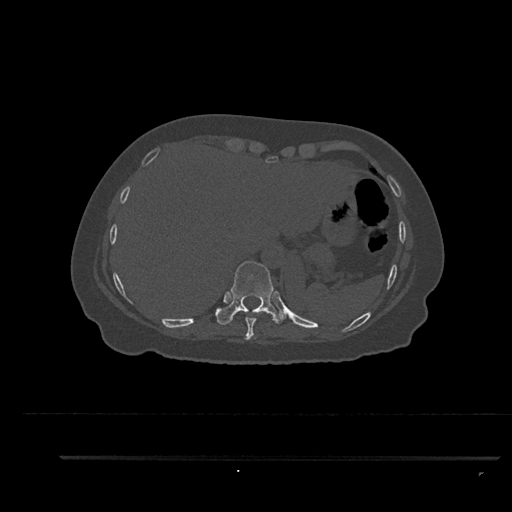
CT including the spine, one axial slice. Position 381 of 797 along the scan axis. Bone window (W 1800 / L 400 HU). 512 × 512 image matrix. Female patient, age 44 years. Case-level facts recorded for this patient, not image findings: primary cancer: renal.
Outlined on this slice (semi-automatic segmentation, software-assisted and operator-edited):
- T10 vertebra: bounding box [x1, y1, x2, y2] px = [216, 261, 285, 325]
- T9 vertebra: [240, 308, 260, 340]